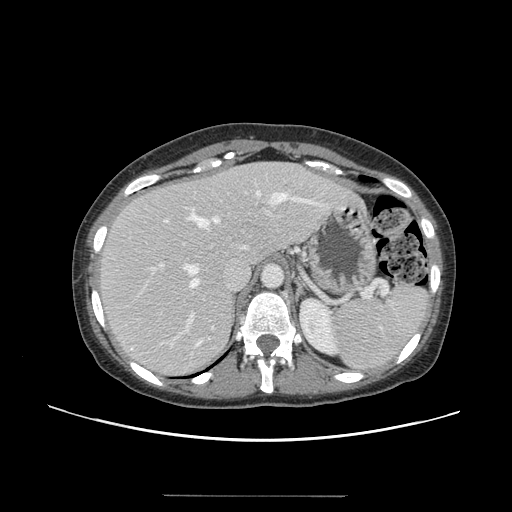
Contrast-enhanced abdominal CT, one axial slice; position 105 of 144 along the scan axis; 120 kVp; intravenous contrast given; soft-tissue window (W 400 / L 40 HU); 2.5 mm slice thickness; 512 × 512 image matrix, field of view 380 × 380 mm. Female patient, age 53 years. From the clinical record (not read from this slice): diagnosis: colorectal cancer liver metastases, imaged before liver resection; multiple liver metastases: yes; largest metastasis: 1.1 cm; disease in both lobes: no.
Outlined on this slice (expert manual segmentation):
- hepatic veins: bounding box <184,191,312,287> (left, top, right, bottom; pixels)
- liver: <98,162,358,376>
- planned liver remnant (the part of the liver to remain after resection): <97,162,300,301>
- portal vein (with intrahepatic branches): <150,210,270,318>